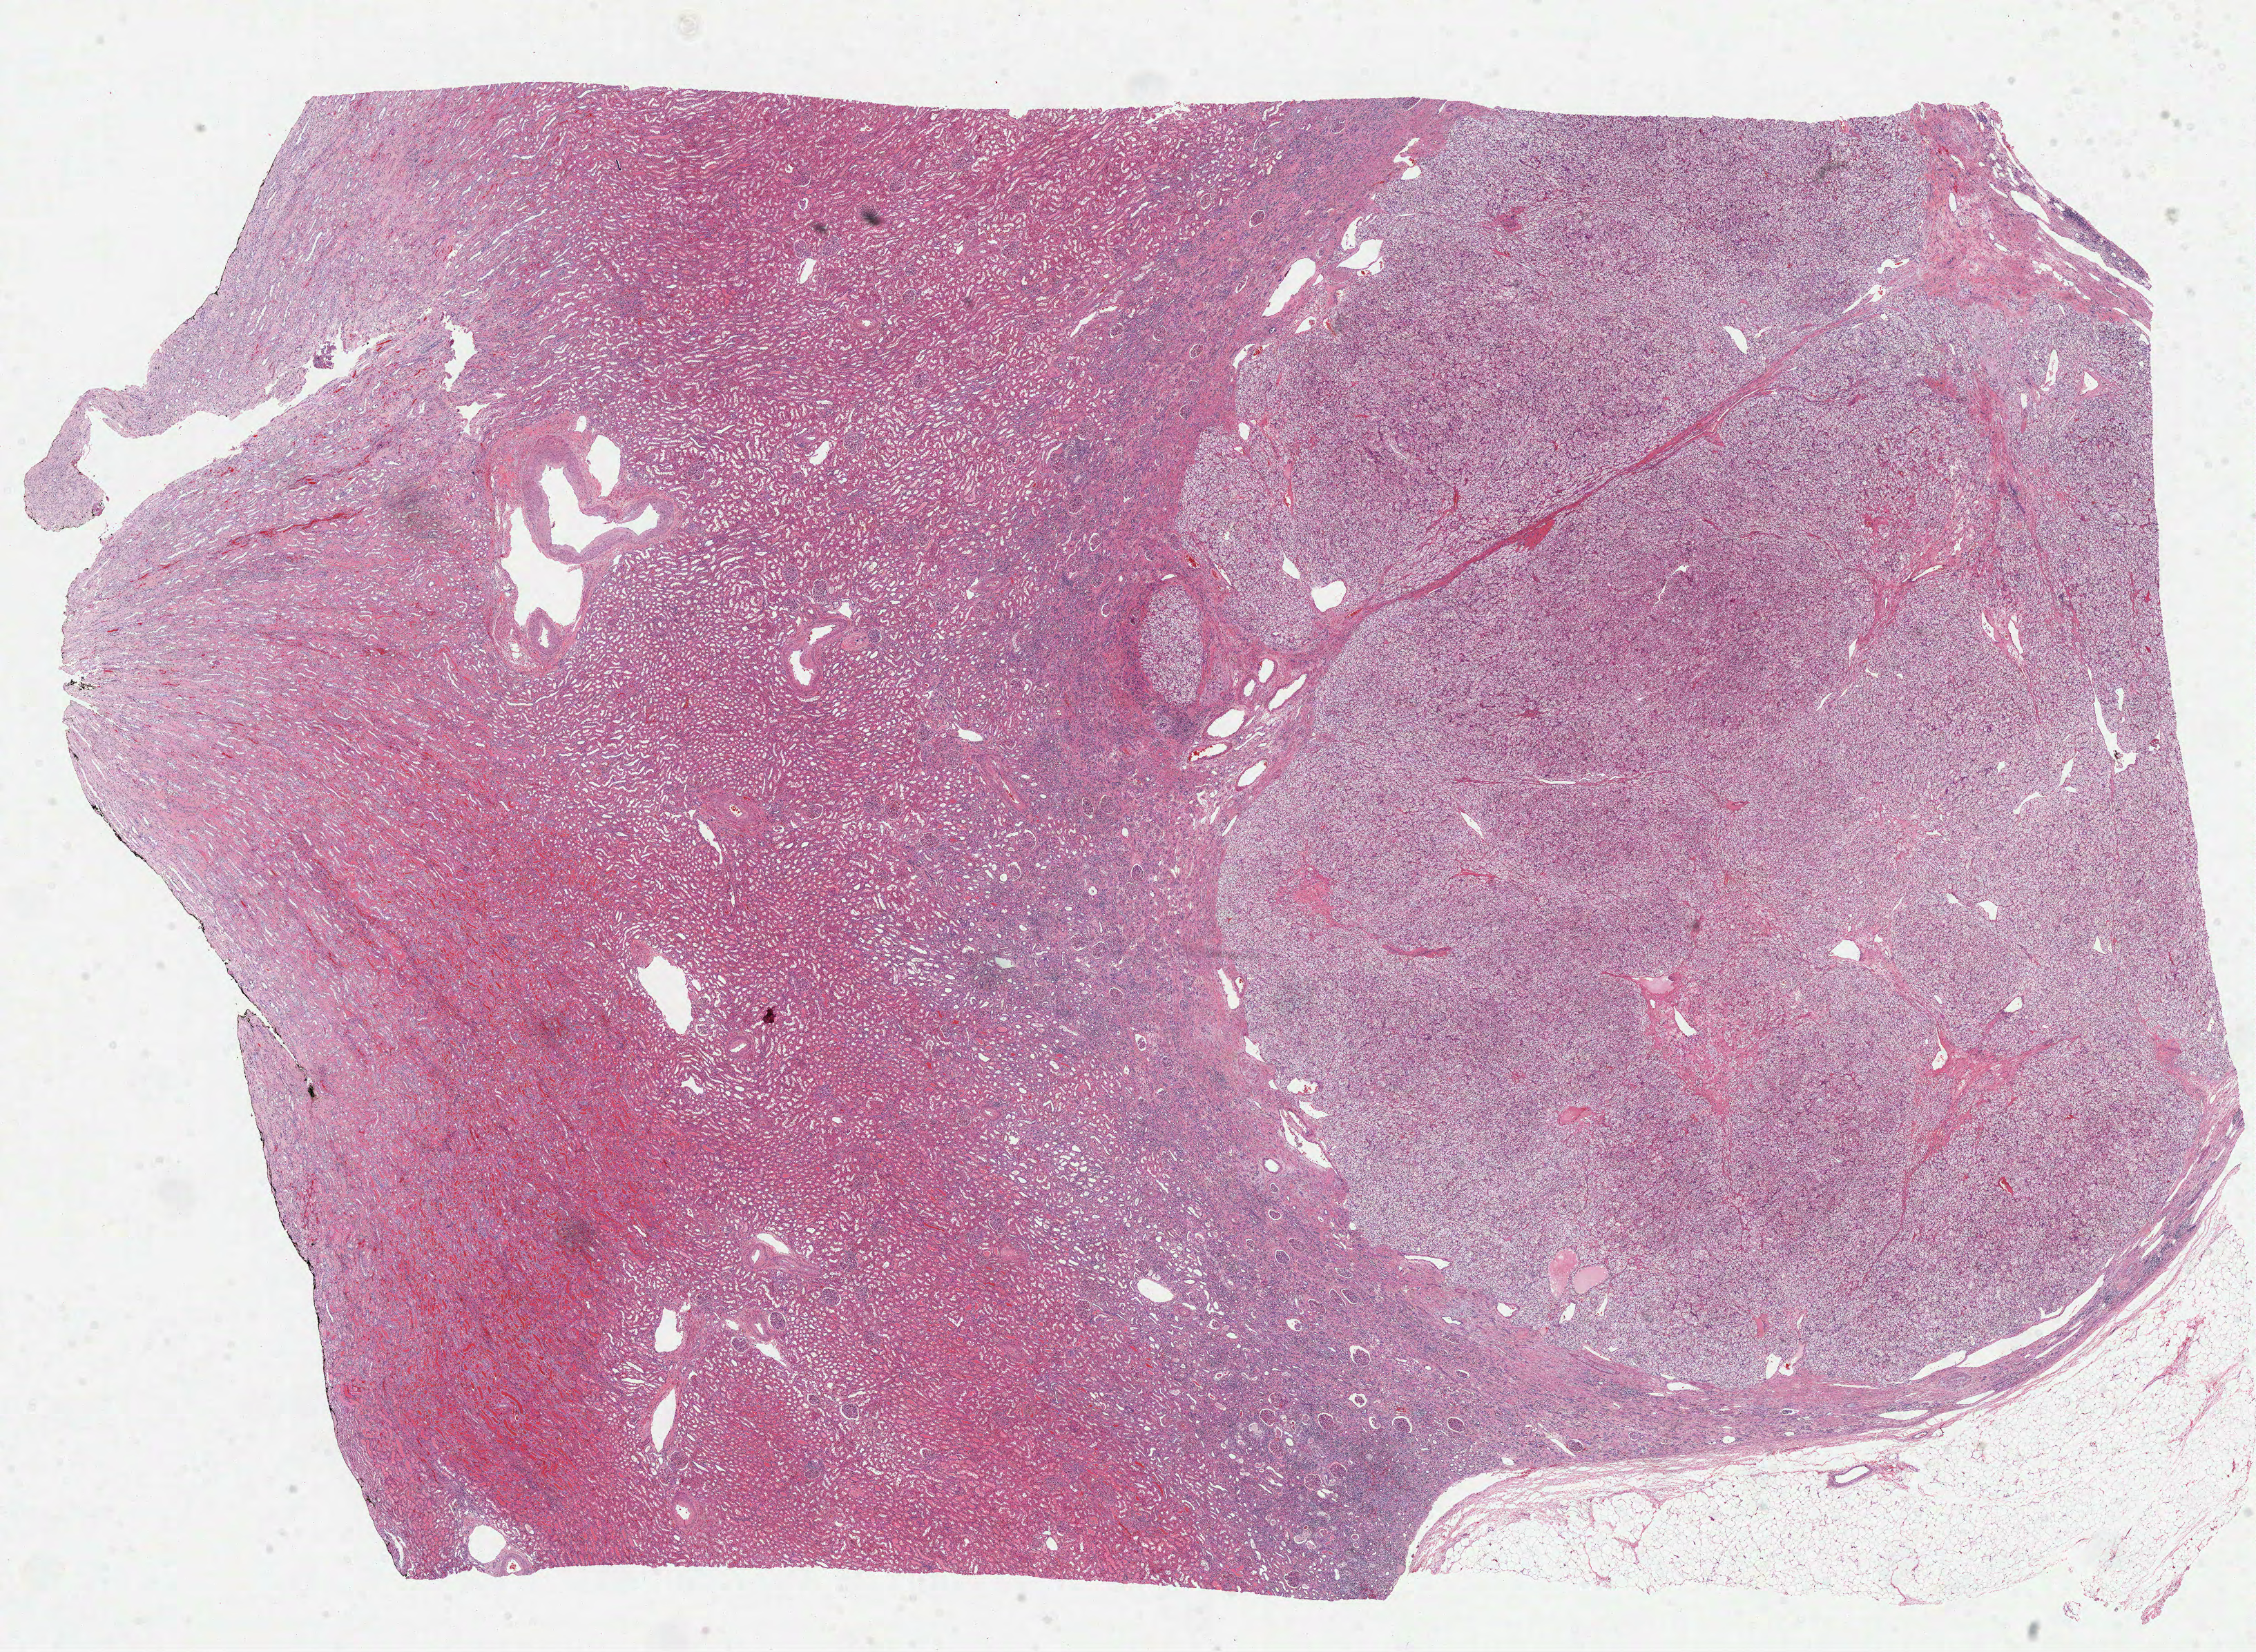
Digitized H&E-stained tissue section (whole slide) — shown as a low-resolution overview of the whole scanned area (about 26.3 x 19.3 mm). FFPE section. Kidney, primary tumour sample. Male, age 53 years at initial diagnosis. Histologic grade: G3 (poorly differentiated).
• TNM: T1b NX M0
• AJCC pathologic stage: I (6th edition)
• pathologic diagnosis: Clear cell adenocarcinoma, NOS